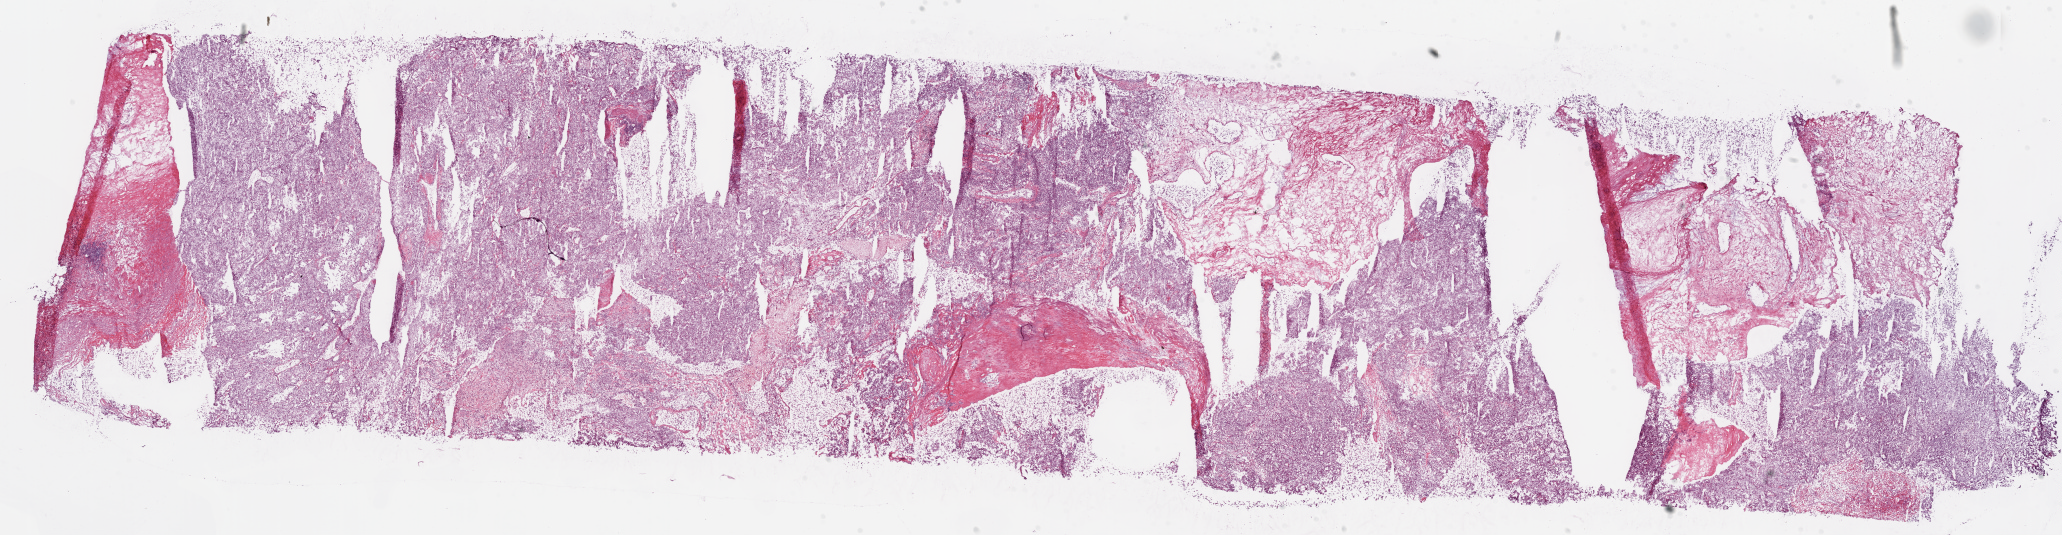
H&E whole-slide image — shown as a low-resolution overview of the whole scanned area (about 33.1 x 8.6 mm, slide scanned at 20x); frozen section from the bottom of the tissue portion; kidney, primary tumour sample. Patient: female, age at initial diagnosis 72 years. Histologic grade: G3 (poorly differentiated). Composition of this section per pathologist review: tumour cells 75%, tumour nuclei 85%, normal cells 0%, stromal cells 25%, necrosis 0%.
- TNM: T3a NX M0
- AJCC pathologic stage: III
- pathologic diagnosis: Clear cell adenocarcinoma, NOS